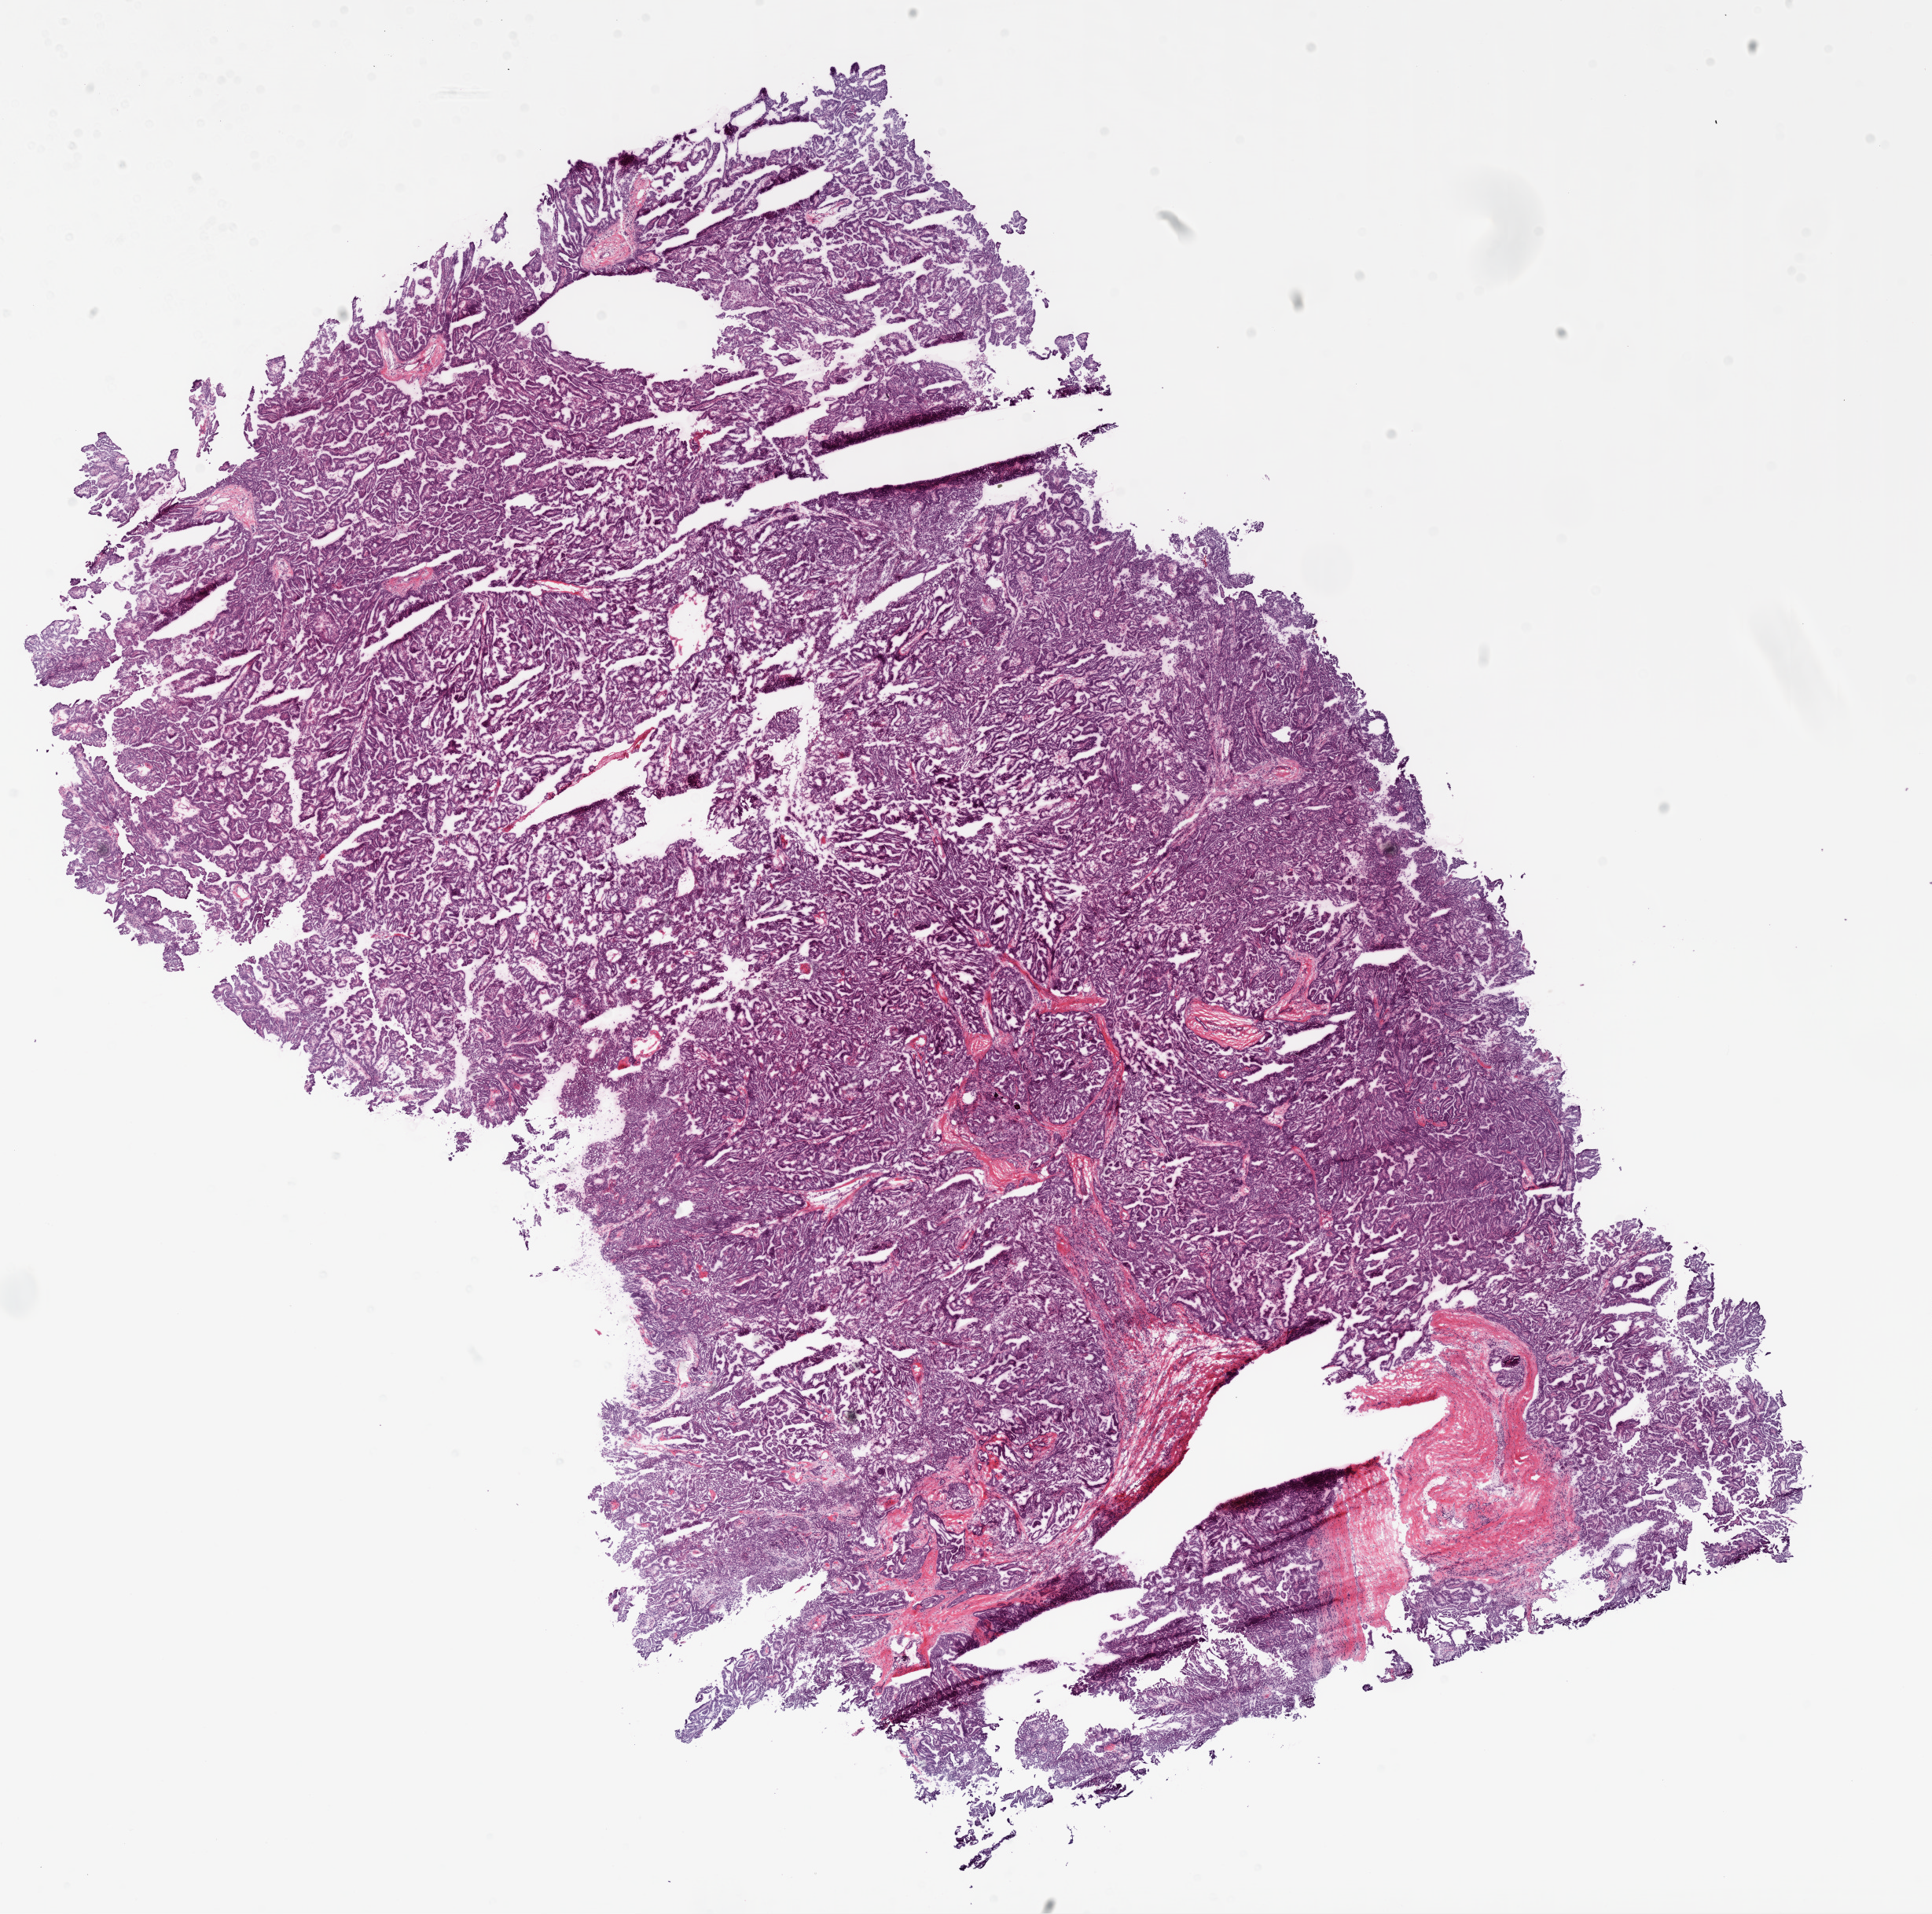
H&E-stained whole-slide image — whole scanned area (about 19.8 x 19.6 mm, slide scanned at 20x) shown as a low-resolution overview; frozen section from the top of the tissue portion; primary tumour sample from the ovary. Patient: female, age at initial diagnosis 48 years. Histologic grade: G3 (poorly differentiated). Pathologist review of this section (percent, as recorded): tumour cells 85%, tumour nuclei 88%, normal cells 10%, stromal cells 2%, necrosis 3%. Infiltration values recorded for this section: lymphocyte infiltration 80%, neutrophil infiltration 20%.
FIGO stage: IIIC. Pathologic diagnosis: Serous cystadenocarcinoma, NOS.